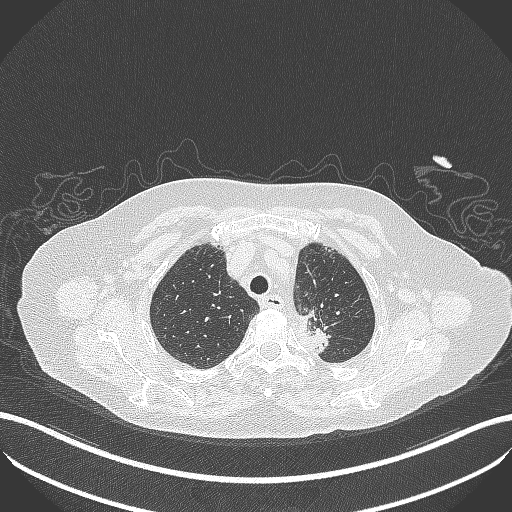
Chest CT, one axial slice; 100 kVp; lung window (W 1500 / L -600 HU); 1 mm slice thickness; 512 × 512 image matrix. Female patient, age 81 years. Case-level facts recorded for this patient, not image findings: clinical TNM (as recorded): T2a N0 M0.
Structures marked on this image (rectangle marked by the reading radiologist):
- lung tumour (recorded histology: adenocarcinoma): bounding box [x1, y1, x2, y2] px = [297, 306, 339, 359]